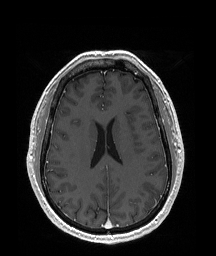
Brain MRI from a brain-tumour surgery series, one axial slice. Position 81 of 192 along the scan axis. T1-weighted post-contrast. 1 mm slice thickness. 216 × 256 image matrix. Case-level facts recorded for this patient, not image findings: histopathology: Glioblastoma; WHO grade: 4; IDH mutation: no.
Structures marked on this image (outlined manually by an expert reader):
- tumour: bounding box <141,182,164,207> (left, top, right, bottom; pixels)